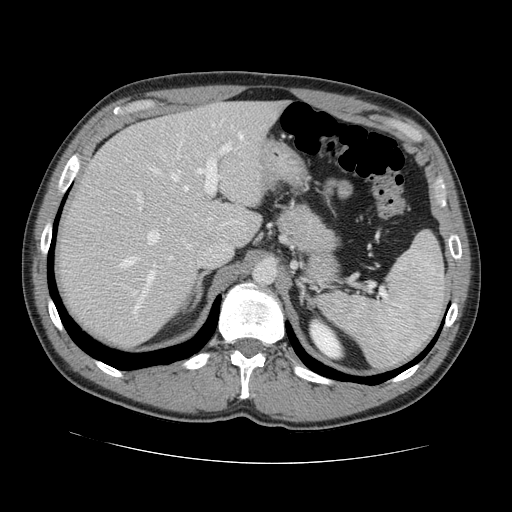
Contrast-enhanced abdominal CT, one axial slice. Position 93 of 131 along the scan axis. 120 kVp. Intravenous contrast given. Soft-tissue window (W 400 / L 40 HU). 512 × 512 image matrix. Male patient, age 40 years. From the clinical record (not read from this slice): diagnosis: colorectal cancer liver metastases, imaged before liver resection; multiple liver metastases: yes; largest metastasis: 2.9 cm.
Structures marked on this image (manually delineated by an expert):
- hepatic veins: box from (x=121, y=135) to (x=243, y=314) px
- liver: (x=60, y=101)–(x=282, y=347)
- planned liver remnant (the part of the liver to remain after resection): (x=99, y=101)–(x=283, y=246)
- portal vein (with intrahepatic branches): (x=132, y=142)–(x=232, y=296)